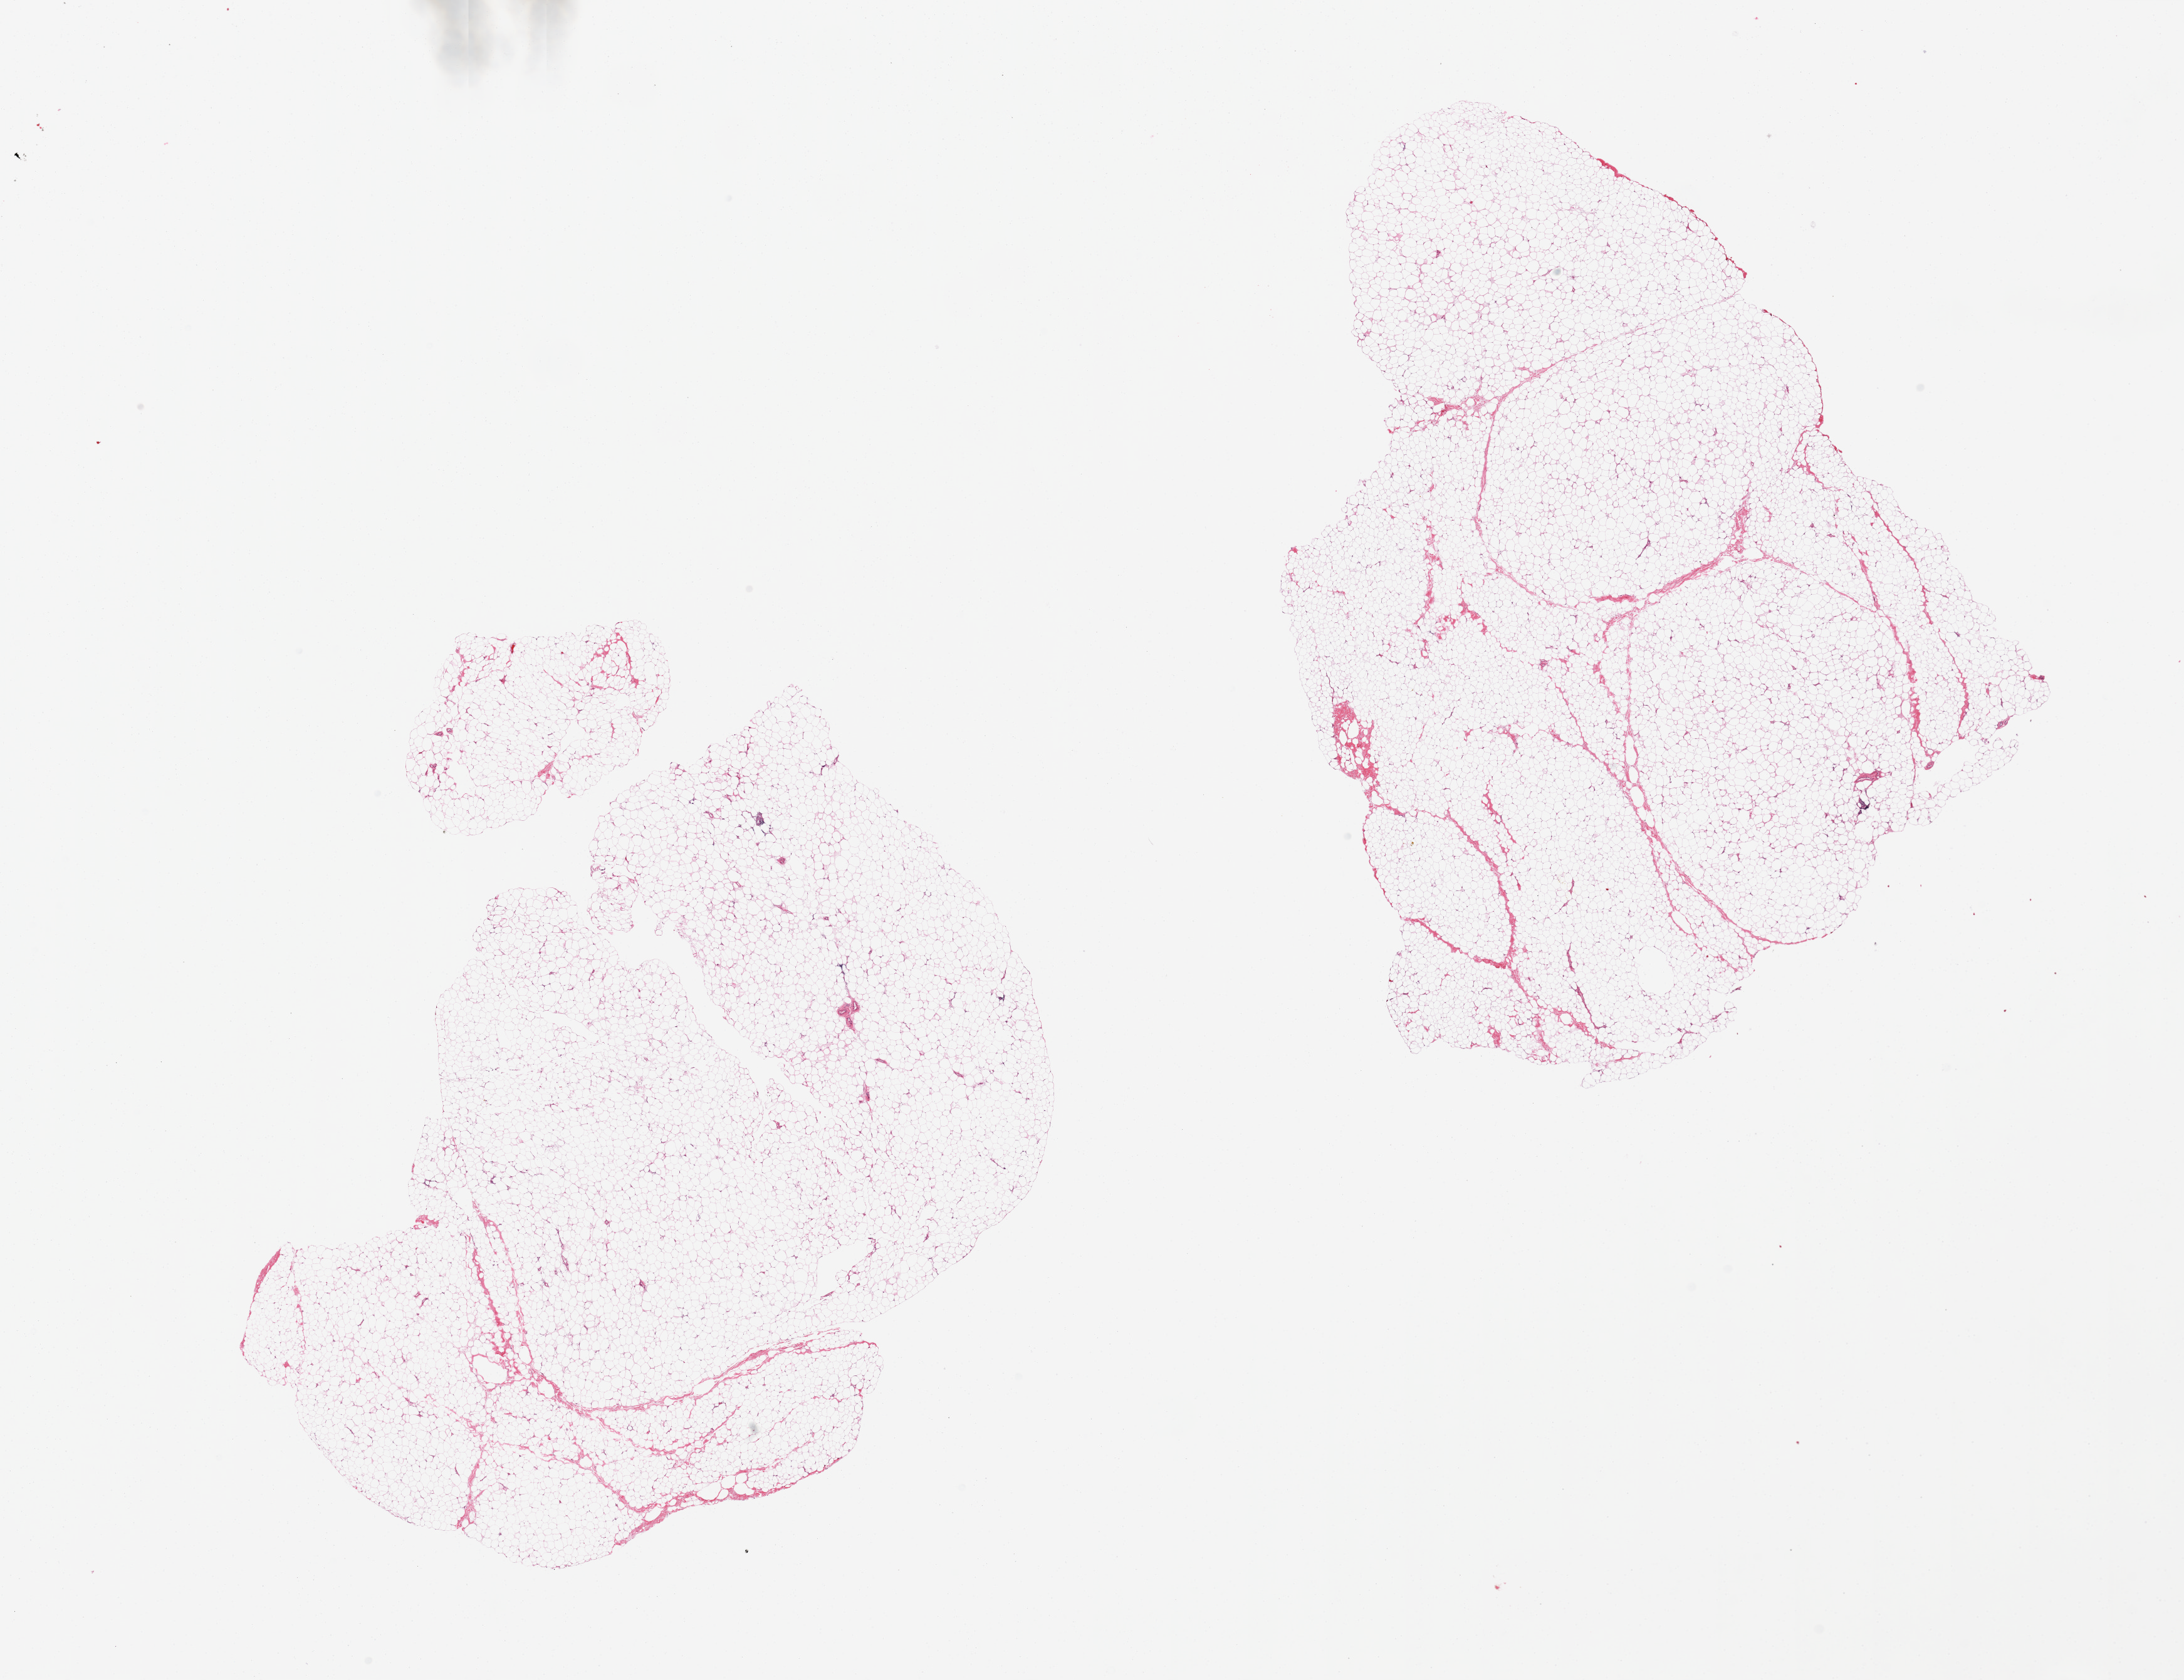
Haematoxylin and eosin whole-slide image, low-resolution overview of the scanned area, about 27.6 x 21.2 mm, PAXgene-fixed paraffin-embedded (PFPE) section, target tissue: breast, donor tissue sample. Male donor.
Pathologist's review note for this sample: 2 pieces, entirely fat.